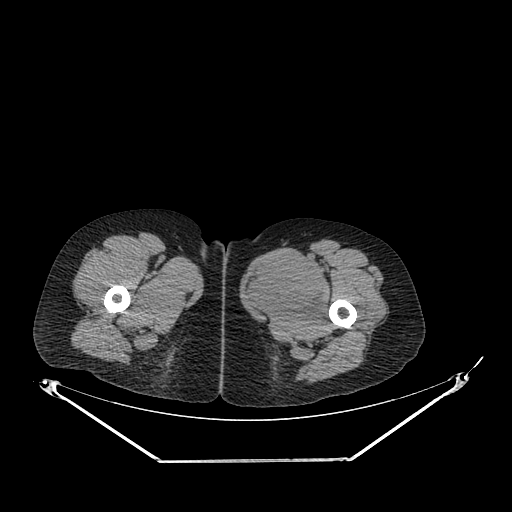
CT of an extremity soft-tissue mass (from a PET/CT study), one axial slice. Slice 249 of 267 in the series (ordered by position). 120 kVp. Soft-tissue window (W 400 / L 40 HU). 3.75 mm slice thickness. 512 × 512 image matrix, field of view 500 × 500 mm. Female patient. Case-level facts recorded for this patient, not image findings: histological type: pleiomorphic leiomyosarcoma; grade: intermediate; site of the primary tumour: left thigh.
Outlined on this slice (expert contour drawn on MRI and transferred to this co-registered scan by the dataset authors):
- gross tumour volume including surrounding oedema: bounding box (x1, y1, x2, y2) in pixels: (244, 253, 325, 318)
- gross tumour volume (mass): (244, 253, 325, 318)